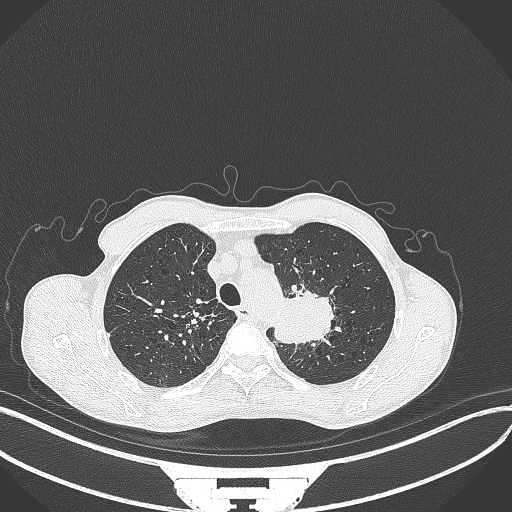
Chest CT, one axial slice; position 336 of 386 along the scan axis; 120 kVp; lung window (W 1500 / L -600 HU); 512 × 512 image matrix, field of view 400 × 400 mm. Patient: male, 65 years. From the clinical record (not read from this slice): clinical TNM (as recorded): T2b N0 M0.
Annotated regions visible in this slice (rectangle marked by the reading radiologist):
- lung tumour (recorded histology: adenocarcinoma): bounding box <269,286,342,350> (left, top, right, bottom; pixels)